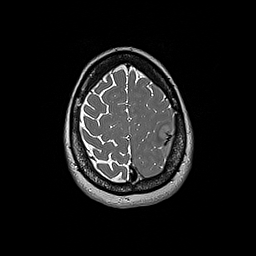
Brain MRI from a brain-tumour surgery series, one axial slice. Slice 52 of 192 in the series (ordered by position). 1 mm slice thickness. 256 × 256 image matrix, field of view 250 × 250 mm. Case-level facts recorded for this patient, not image findings: histopathology: Glioblastoma; WHO grade: 4; IDH mutation: no.
Structures marked on this image (manually delineated by an expert):
- tumour: bounding box [x1, y1, x2, y2] px = [159, 126, 183, 163]